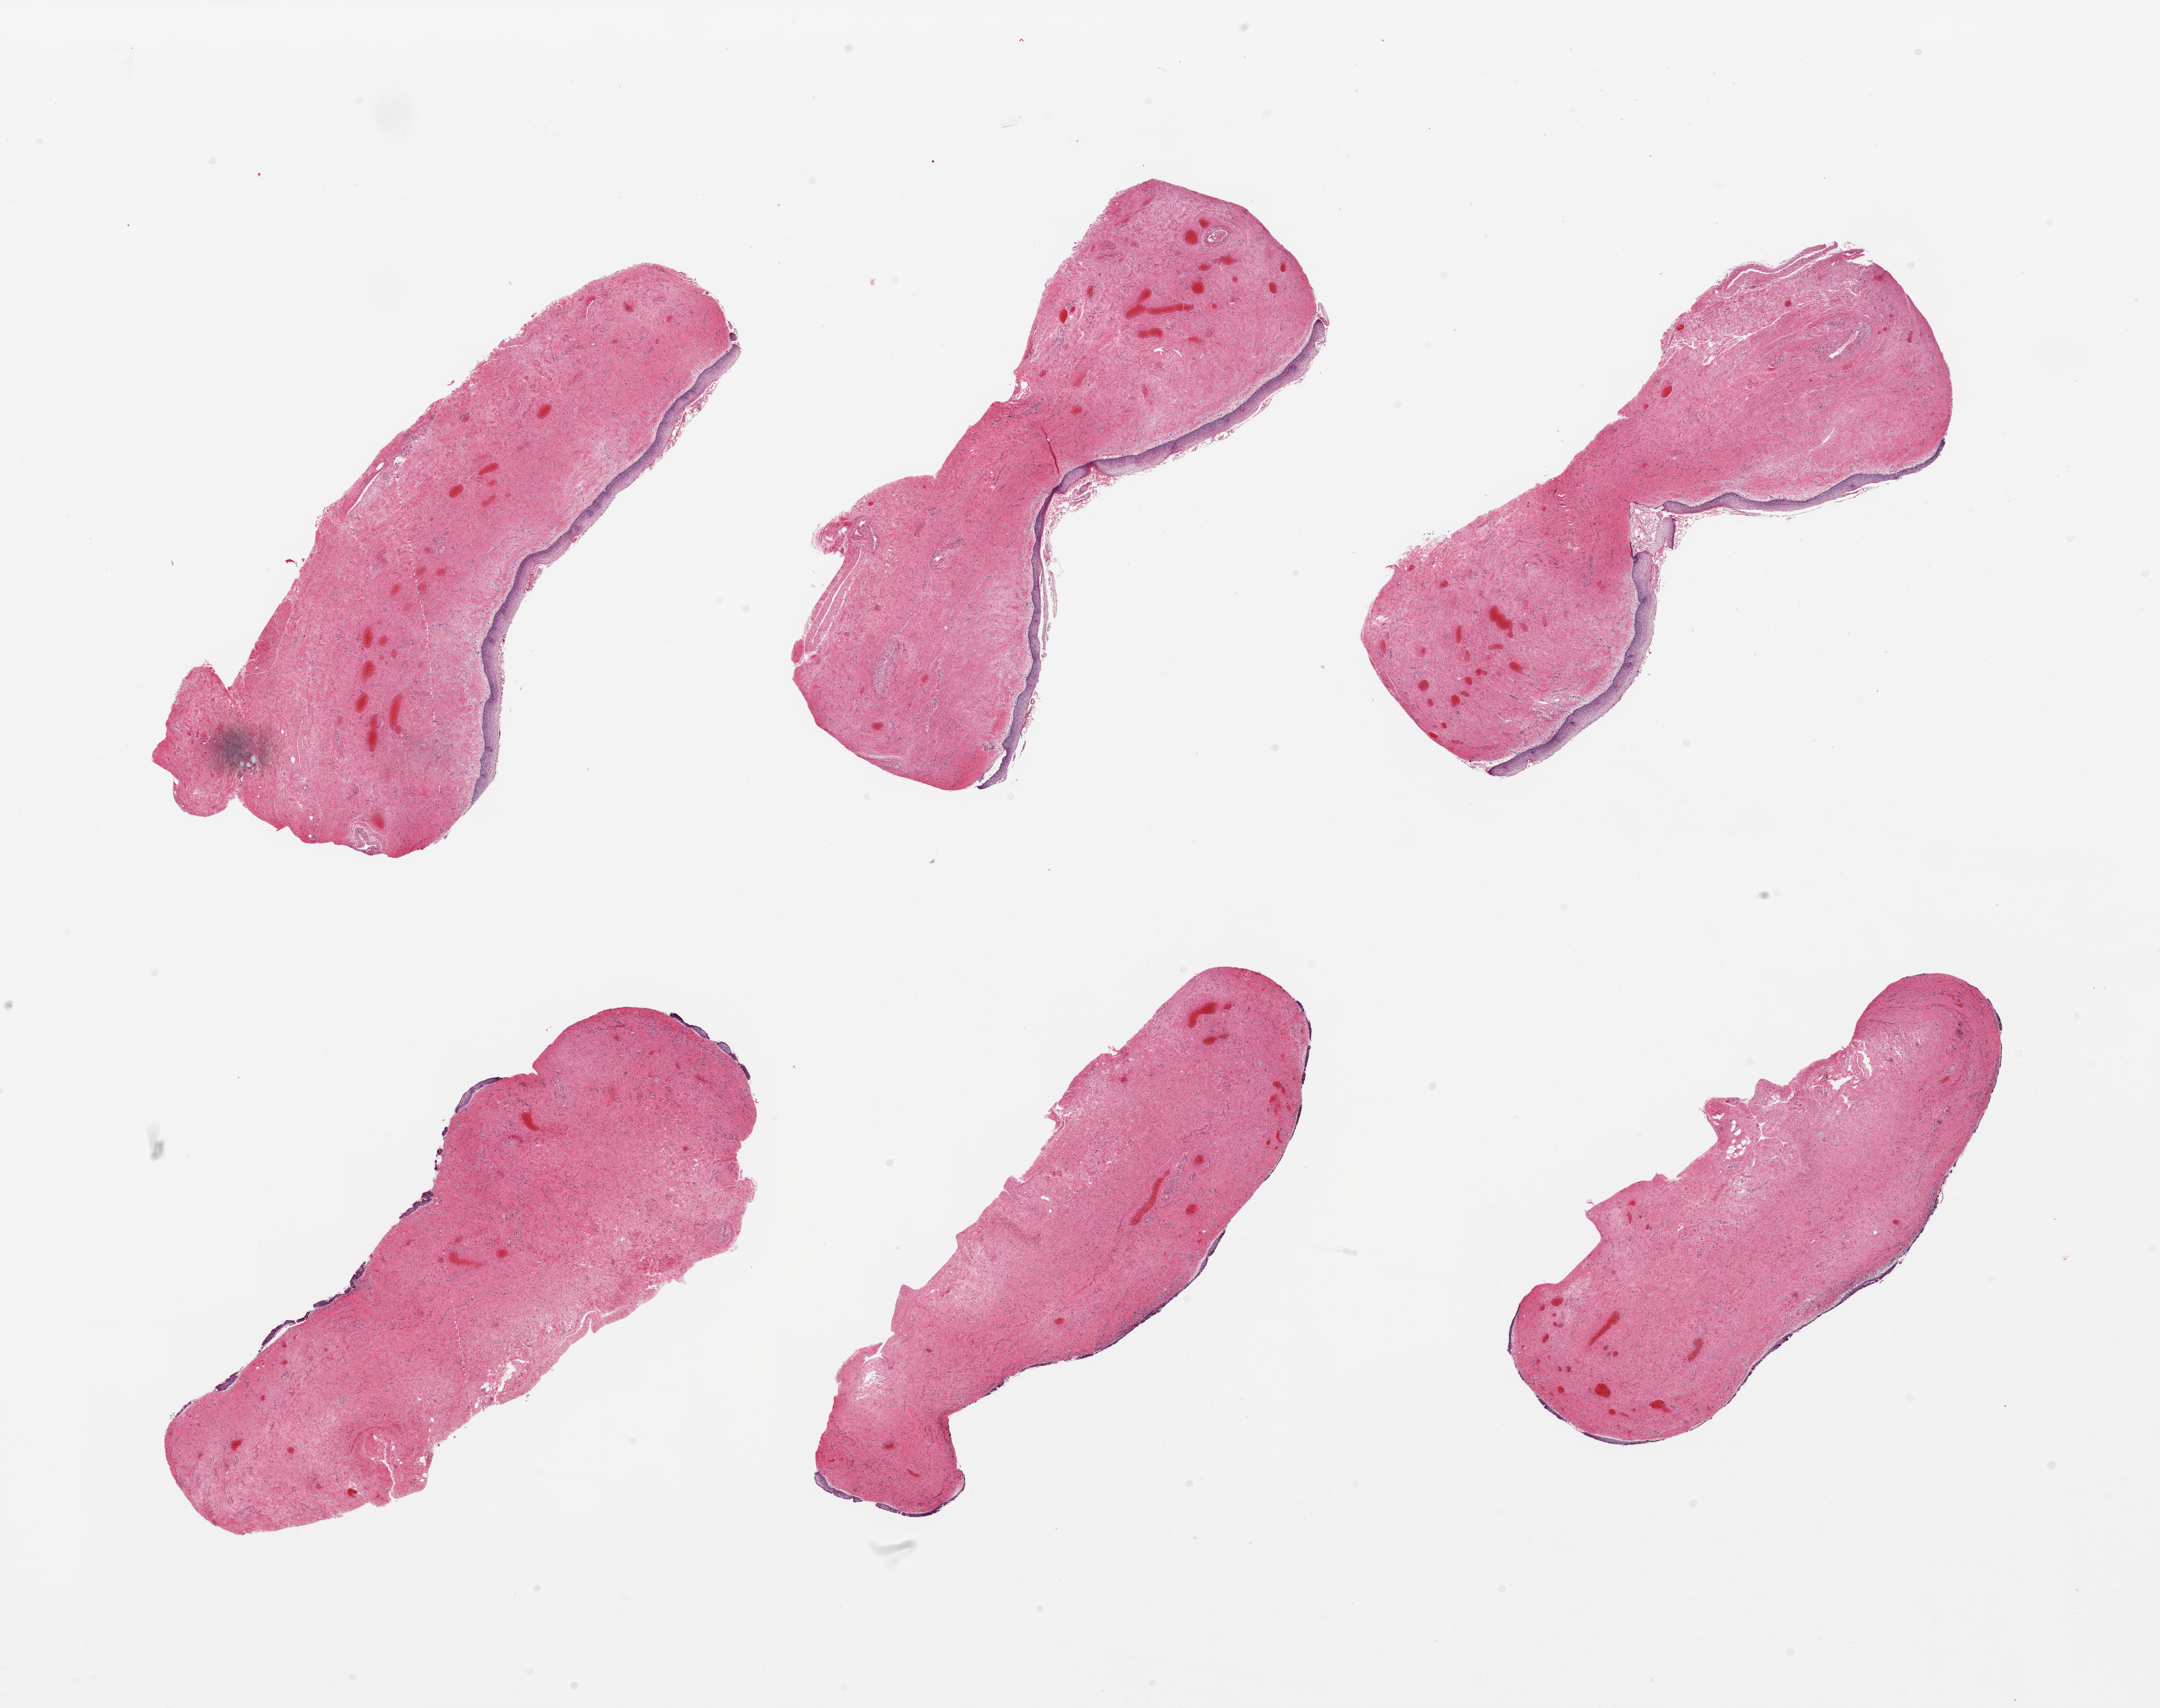
H&E whole-slide image, shown as a low-resolution overview of the whole scanned area (about 24.6 x 19.5 mm). PAXgene-fixed paraffin-embedded (PFPE) section. Section of vagina (target tissue). Donor tissue sample. Donor: female.
Reviewer comment on this tissue sample: 6 pieces; atrophic, partly sloughed epithelium.